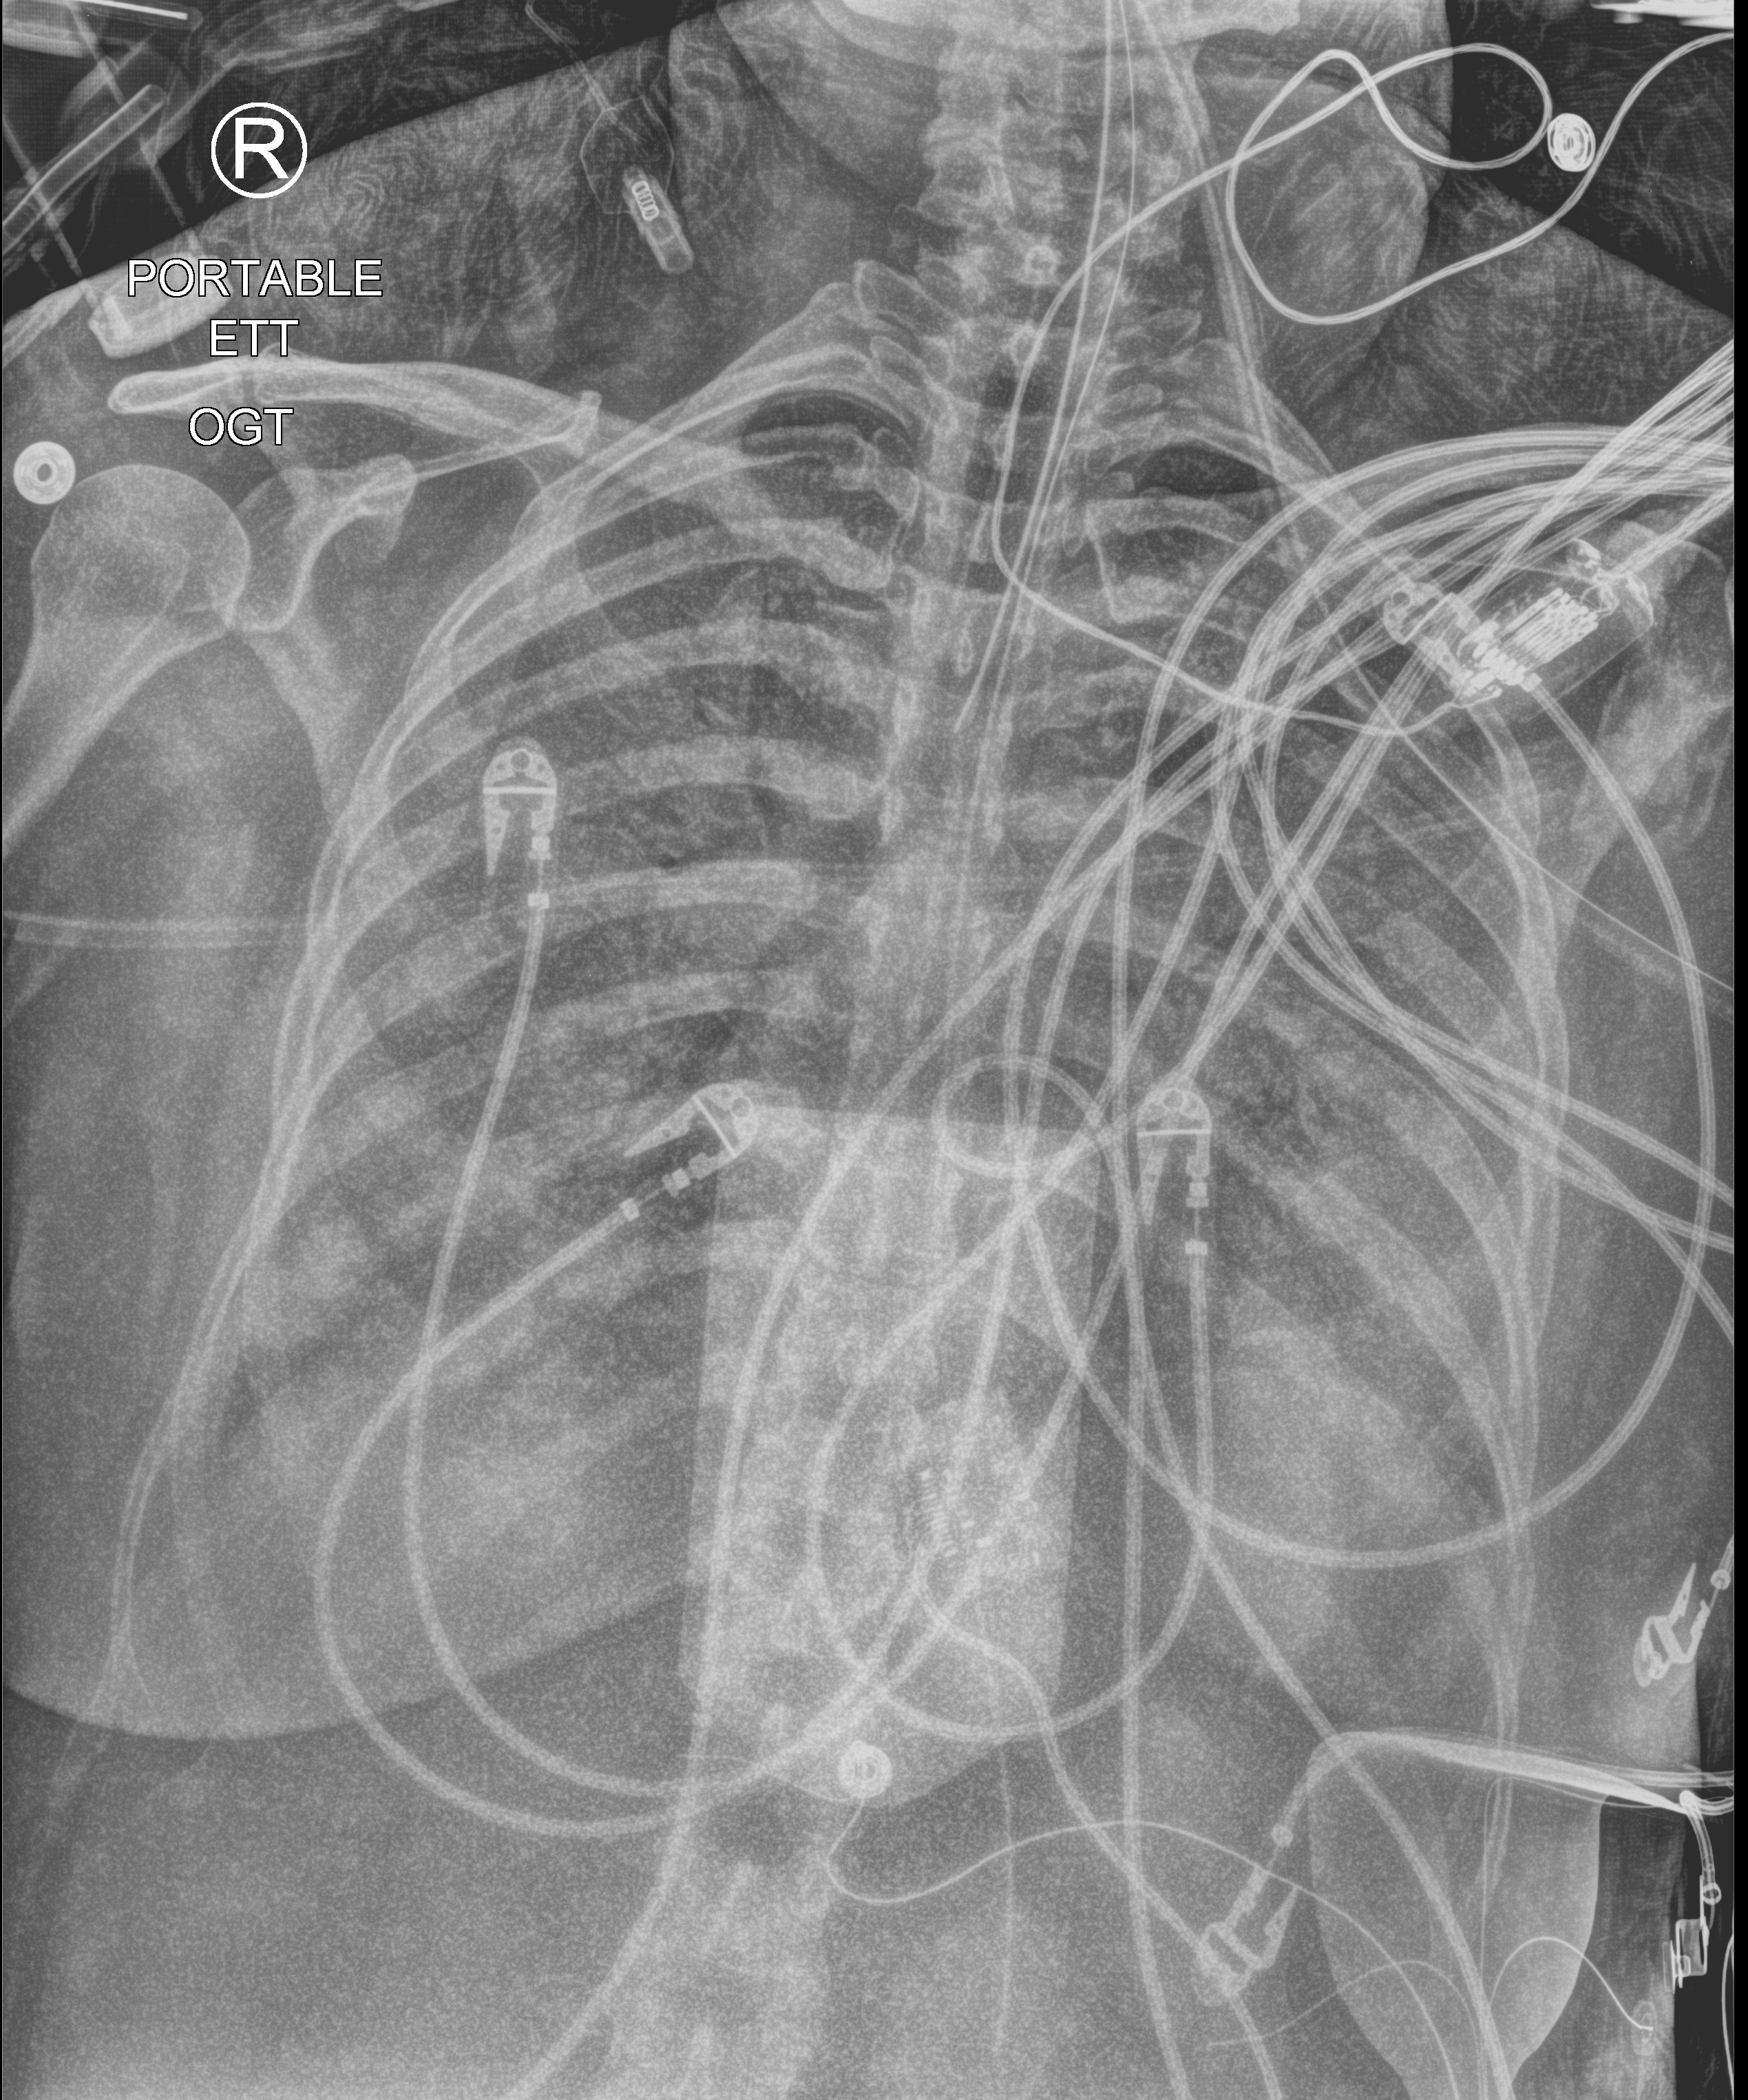
Chest X-ray (portable), anteroposterior (AP) projection. Male patient hospitalised with COVID-19, age 18–59 years.
Admission-level facts for this patient (not findings on this image; timing relative to this image not recorded): admitted to intensive care during this hospital stay: yes; chronic kidney disease (admission record): no.